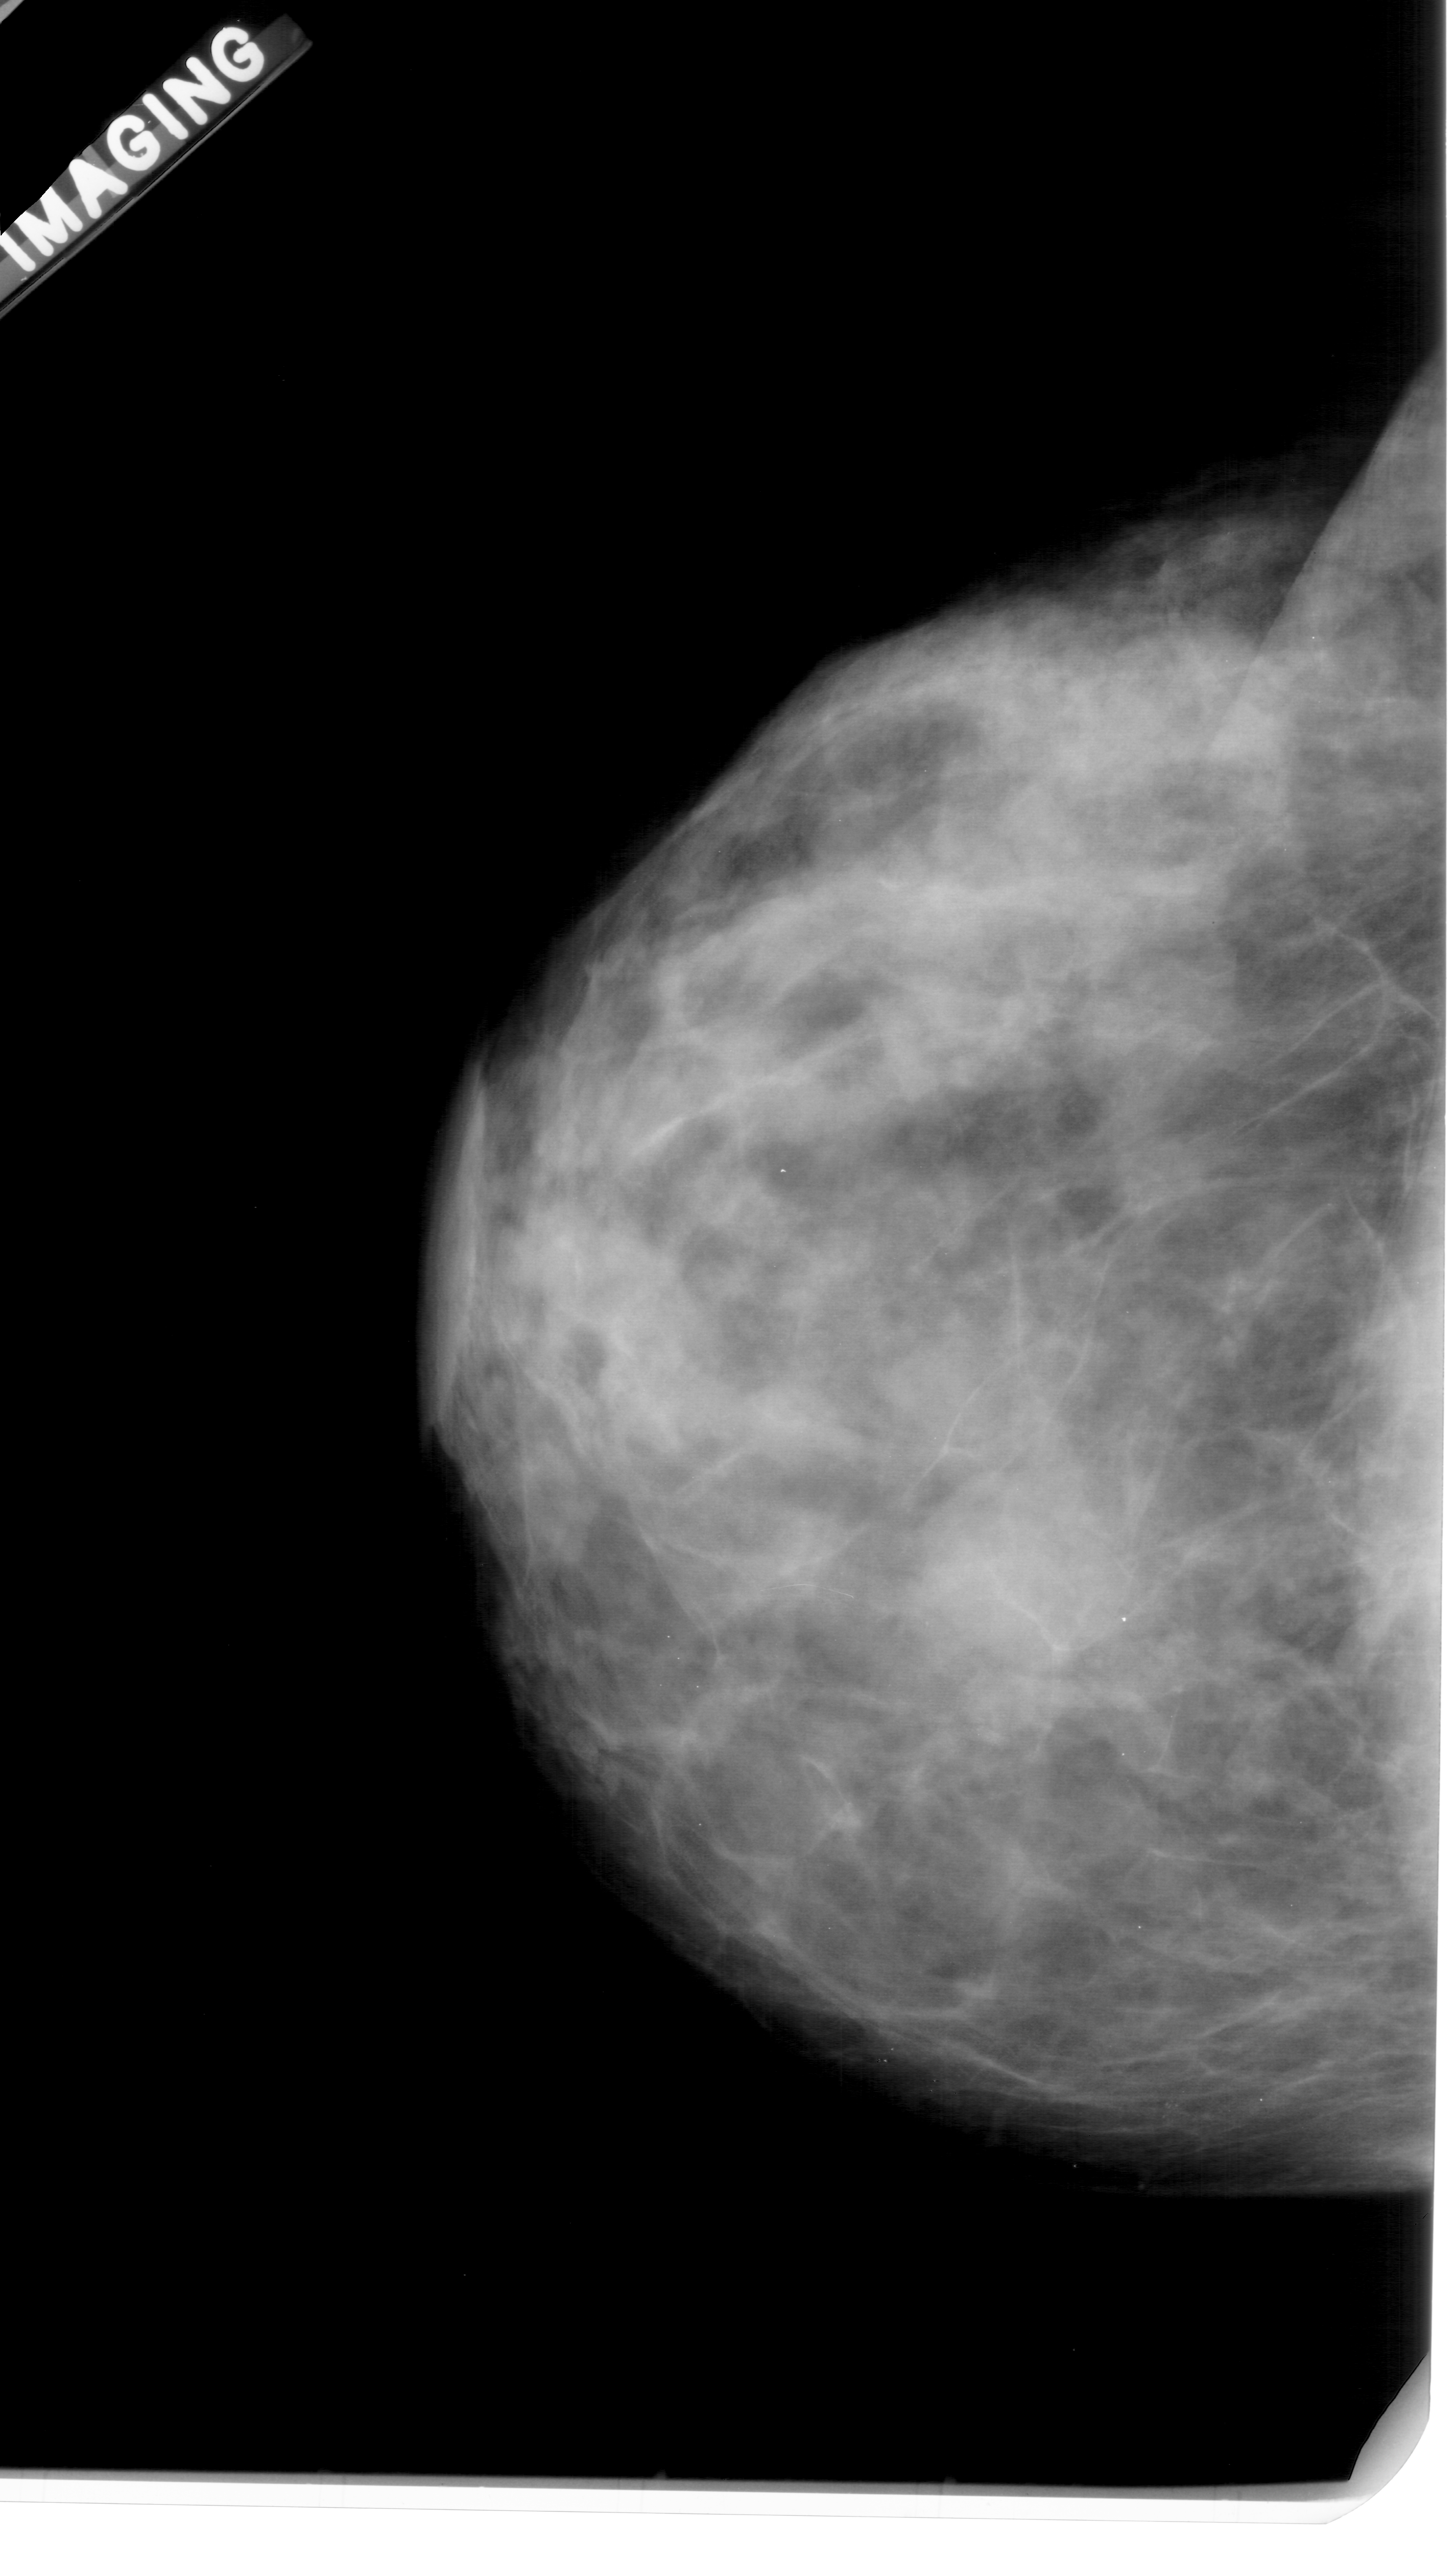
Digitized screen-film mammogram, left breast, craniocaudal (CC) view, breast composition: extremely dense (BI-RADS density category 4 of 4).
- Mass, shape oval, margins obscured; BI-RADS assessment category 3; subtlety rating 2 on a 1 (subtle) to 5 (obvious) scale; pathology (as recorded): benign.